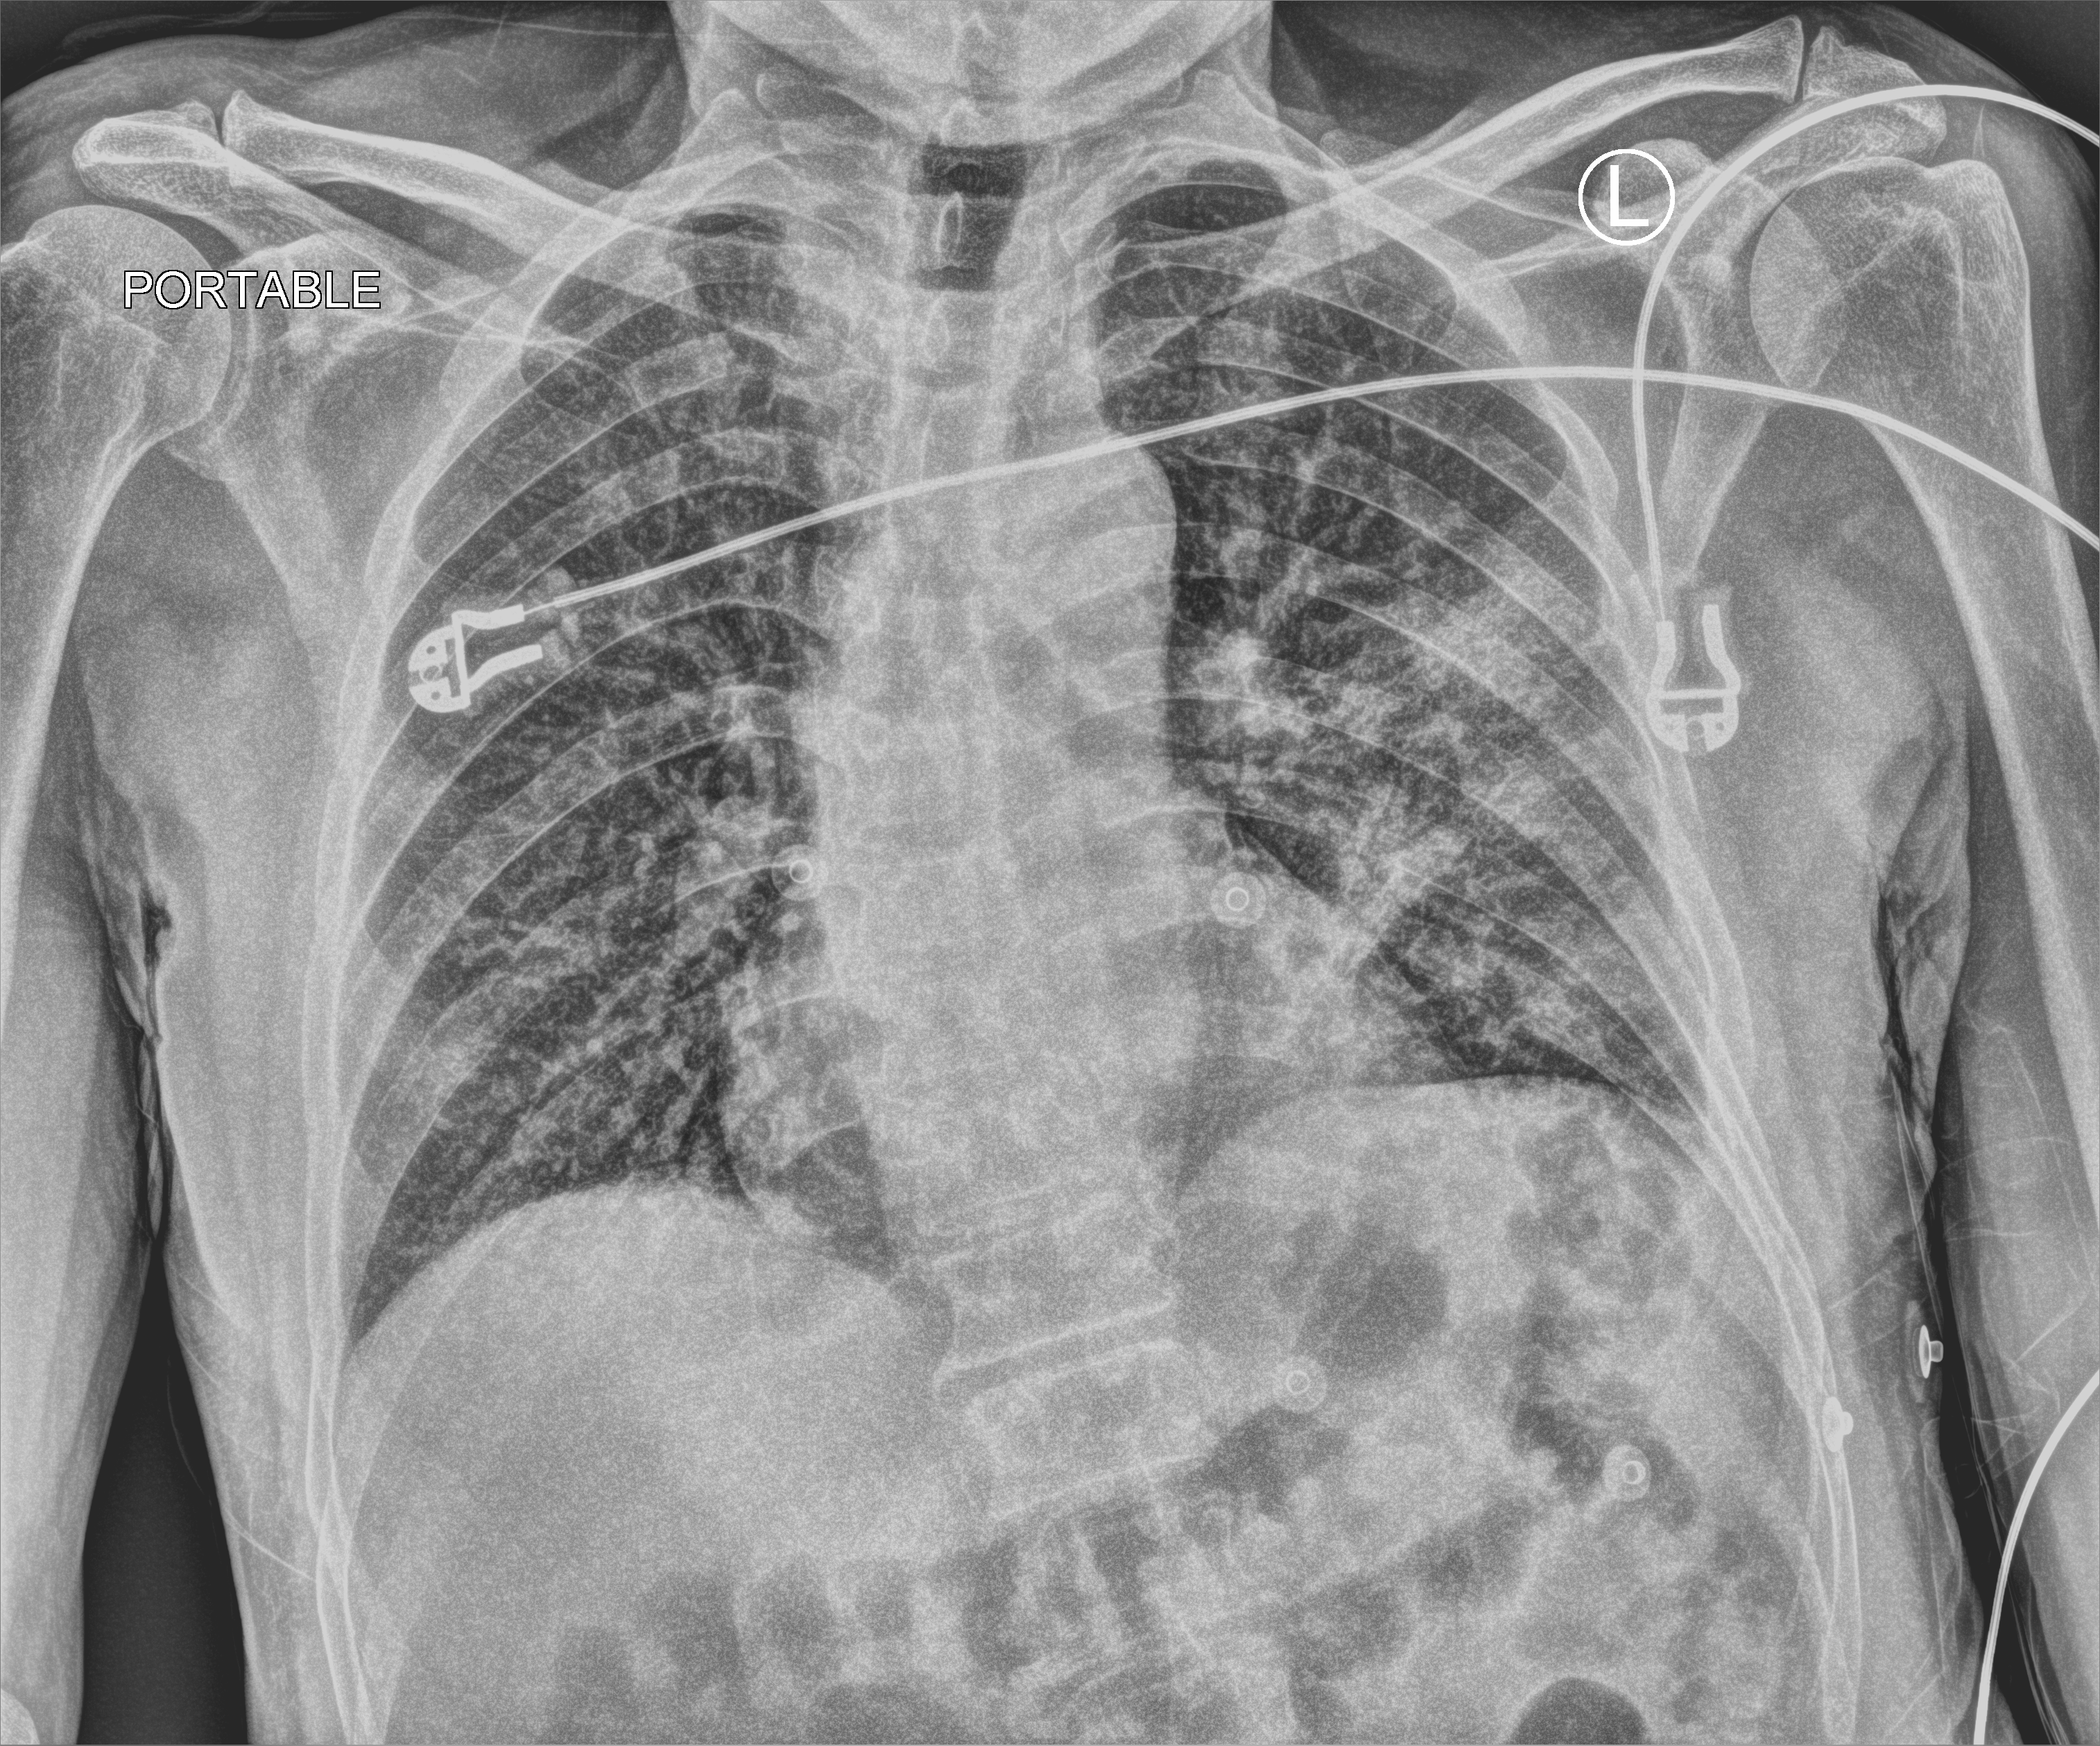
Chest X-ray (portable). Patient hospitalised with COVID-19; male, aged 60–74 years.
Admission-level facts for this patient (not findings on this image; timing relative to this image not recorded): length of hospital stay: 1 day.